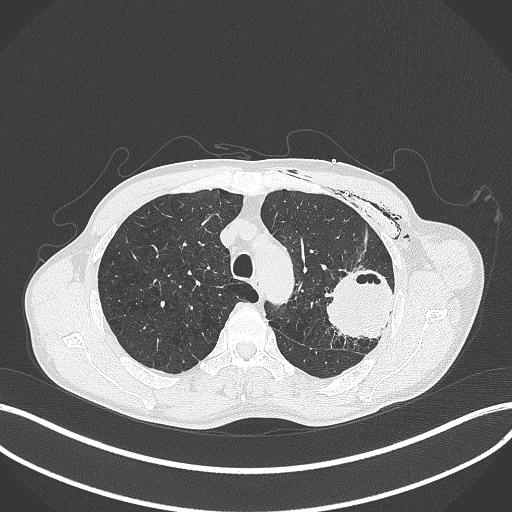
Chest CT, one axial slice. Position 308 of 457 along the scan axis. 120 kVp. Lung window (W 1500 / L -600 HU). 512 × 512 image matrix, field of view 400 × 400 mm. Patient: male, 58 years. Case-level facts recorded for this patient, not image findings: clinical TNM (as recorded): T3 N0 M0.
Annotated regions visible in this slice (bounding box drawn by a radiologist):
- lung tumour (recorded histology: adenocarcinoma): bounding box <326,265,401,345> (left, top, right, bottom; pixels)